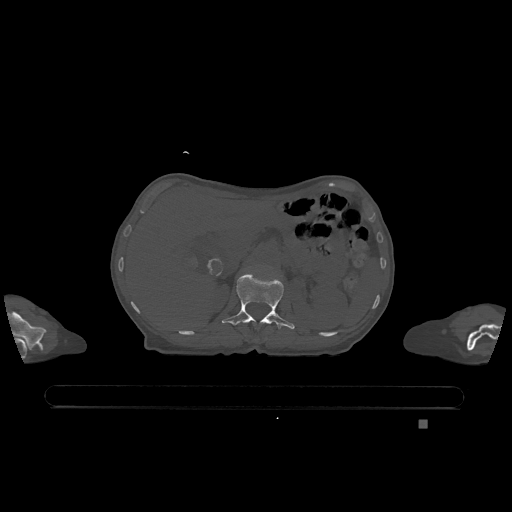
CT including the spine, one axial slice. Position 474 of 1317 along the scan axis. Bone window (W 1800 / L 400 HU). 512 × 512 image matrix, field of view 500 × 500 mm. Patient: female, 74 years. Case-level facts recorded for this patient, not image findings: primary cancer: lung.
Outlined on this slice (semi-automatically segmented with operator editing):
- L1 vertebra: bounding box [x1, y1, x2, y2] px = [222, 272, 295, 329]